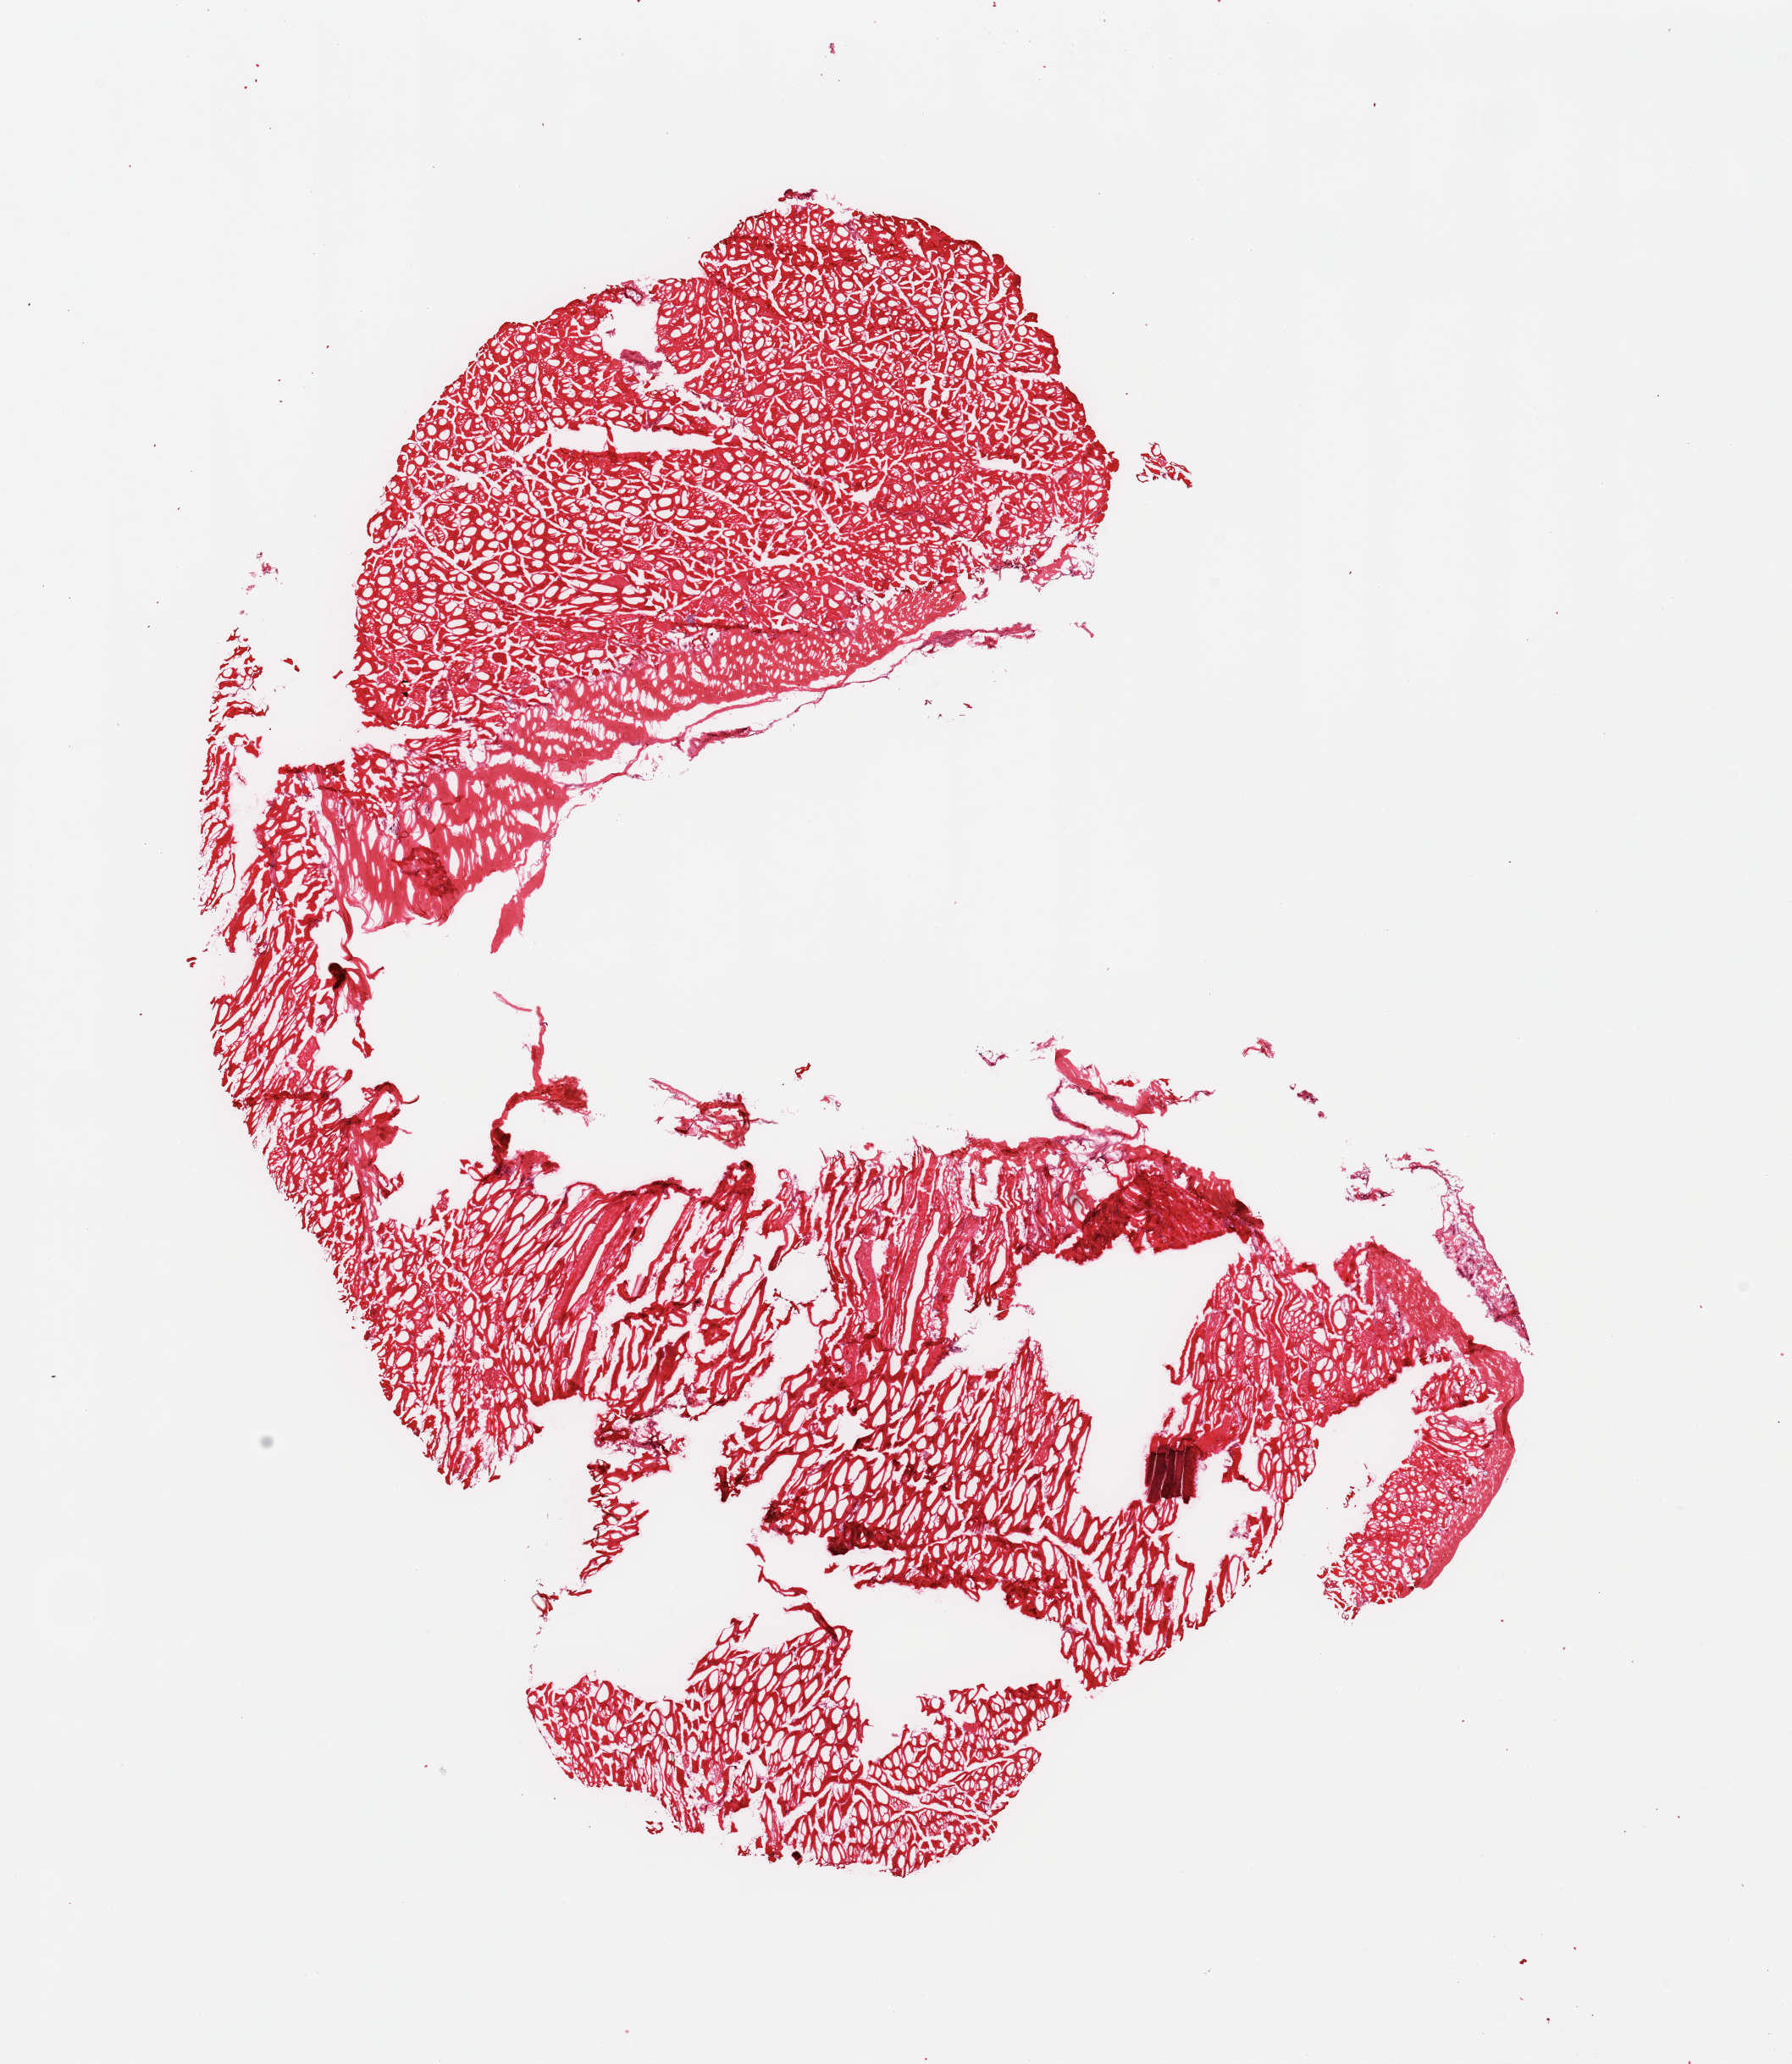
Digitized haematoxylin and eosin-stained section, low-resolution overview of the scanned area, about 16.7 x 19.3 mm (from a 20x scan), frozen section, section of skeletal muscle (target tissue), donor tissue sample. Male donor.
* reviewer comment on this tissue sample: 1 piece